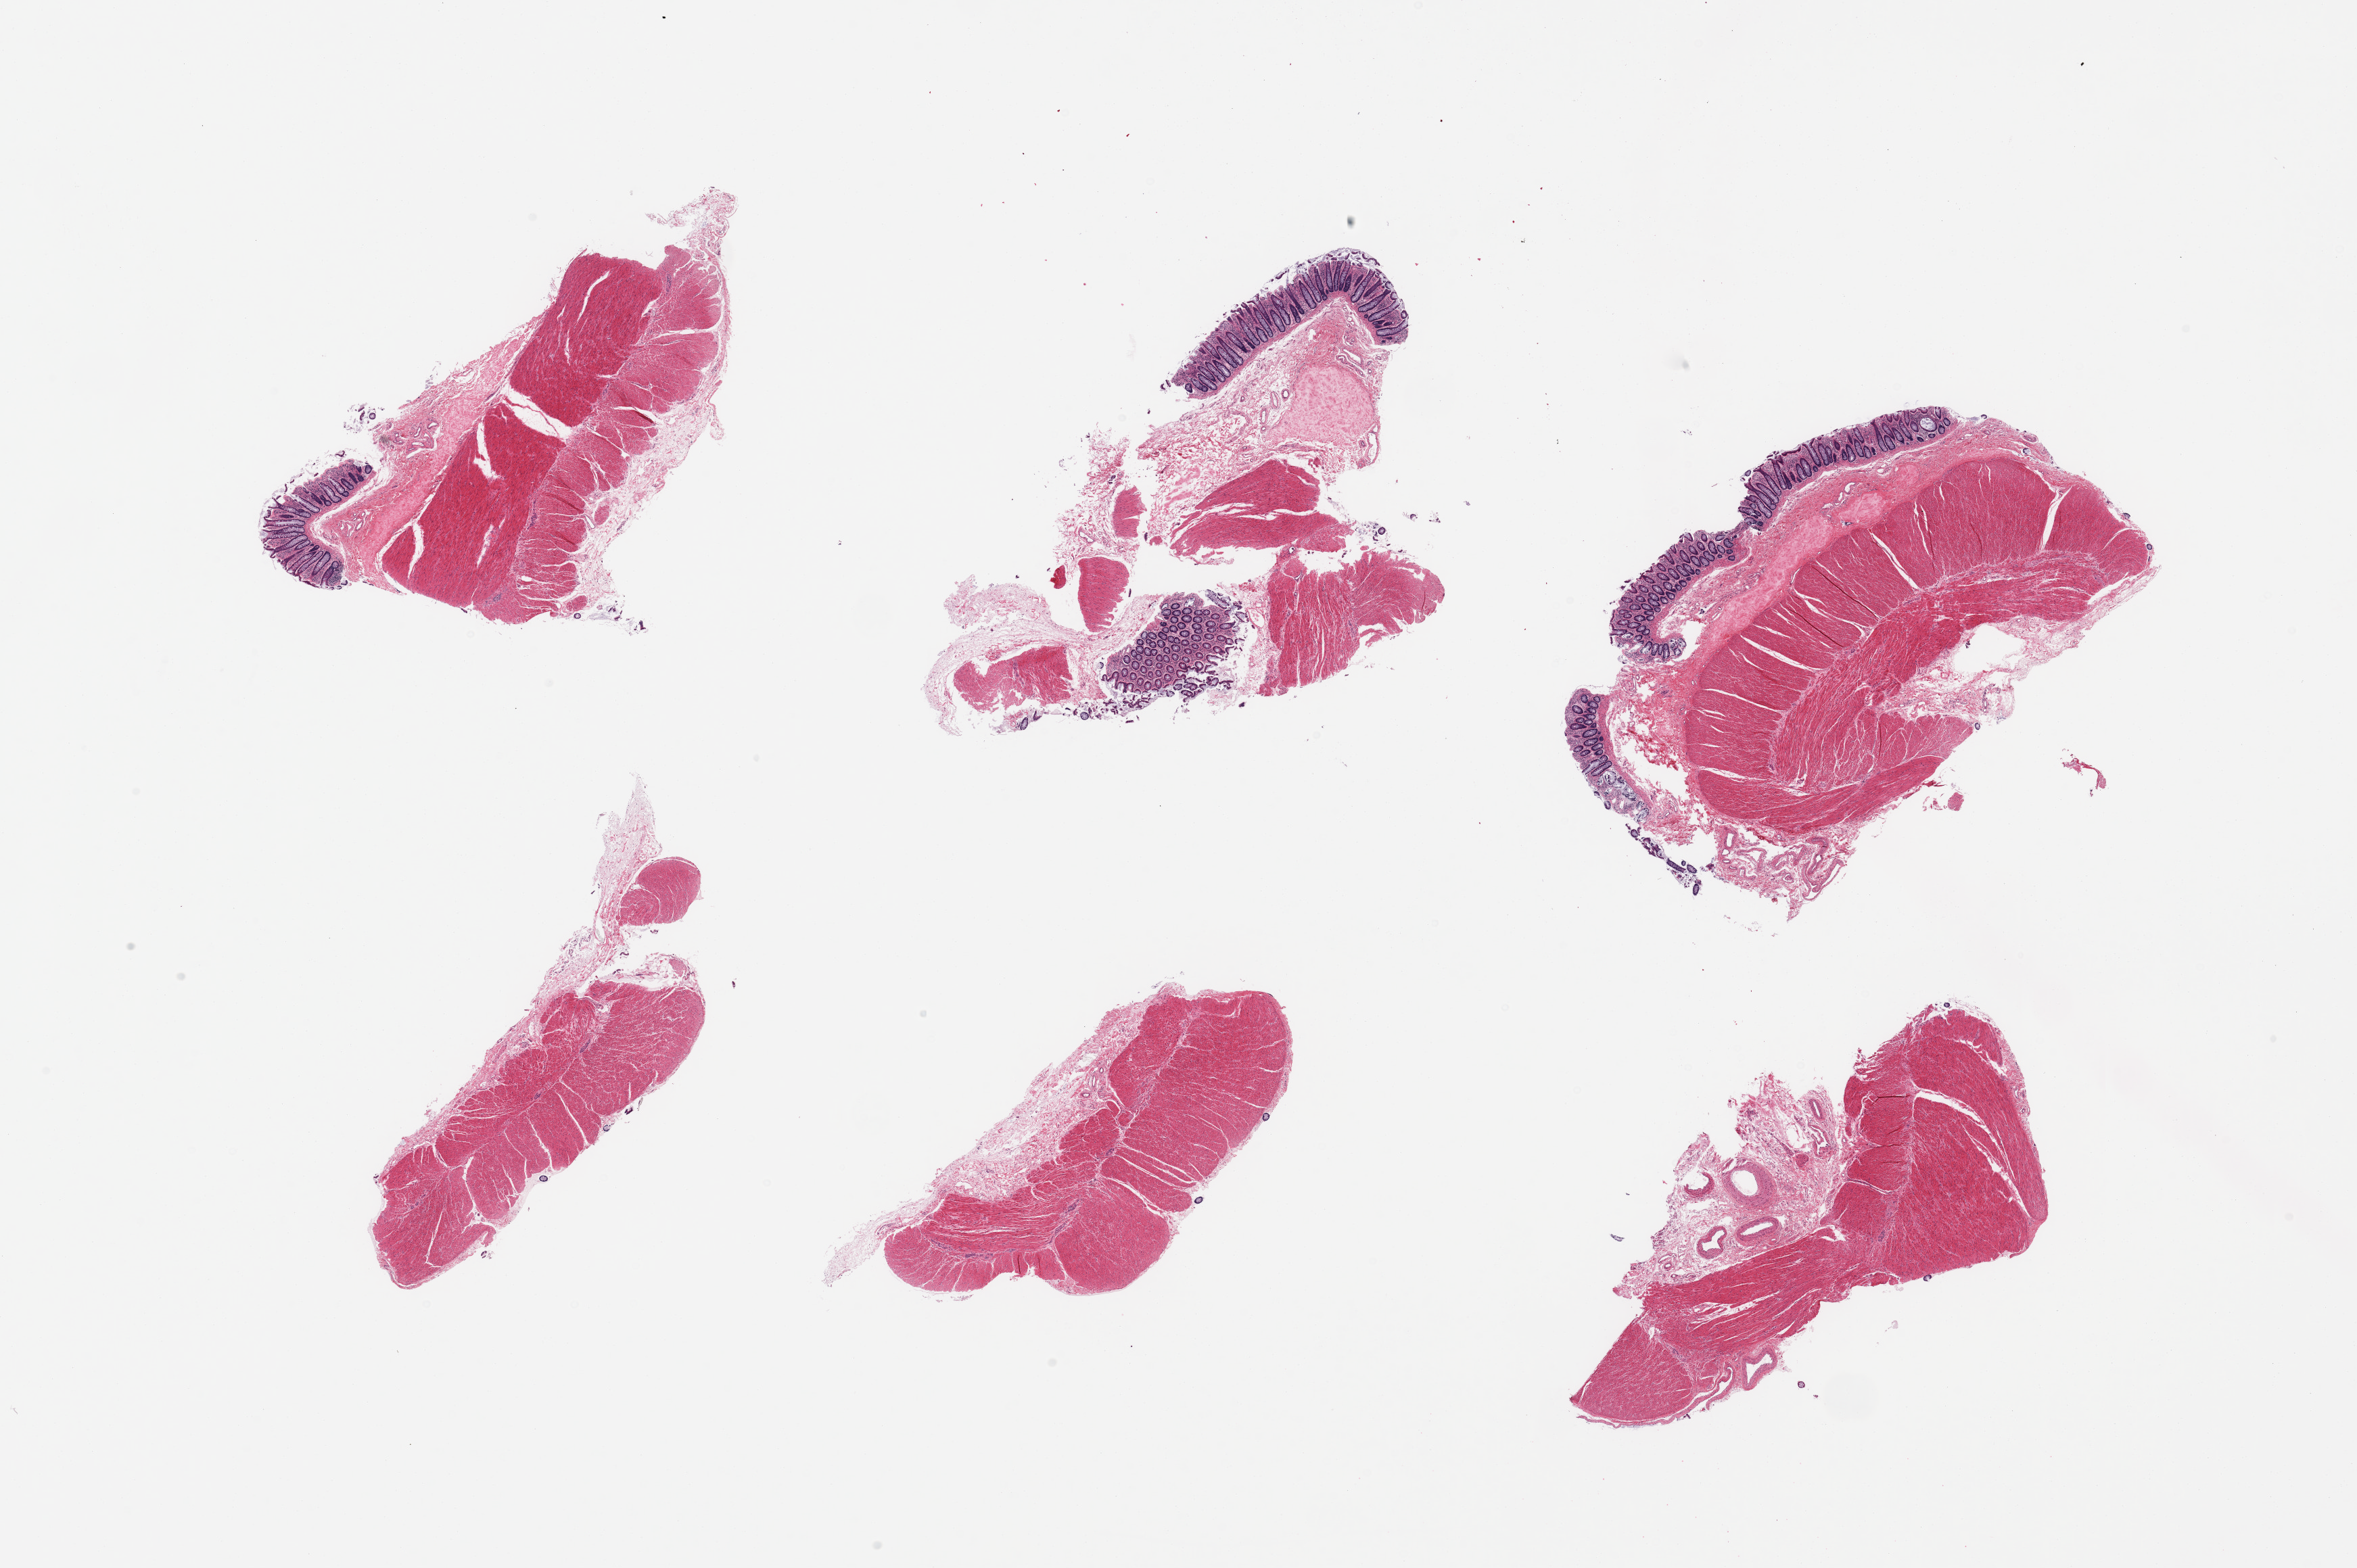
Digitized haematoxylin and eosin-stained section, brightfield, shown as a low-resolution overview of the whole scanned area (about 27.6 x 18.3 mm, from a 20x scan). PAXgene-fixed, paraffin-embedded tissue. Sampled site (target tissue): sigmoid colon. Donor tissue sample.
- review note (as recorded): 6 pieces; 3 pieces have mucosa as well as muscularis; foci of edematous, amyloid-like stroma or fibroelastosis in submucosa of 3 pieces (as in transverse colon)